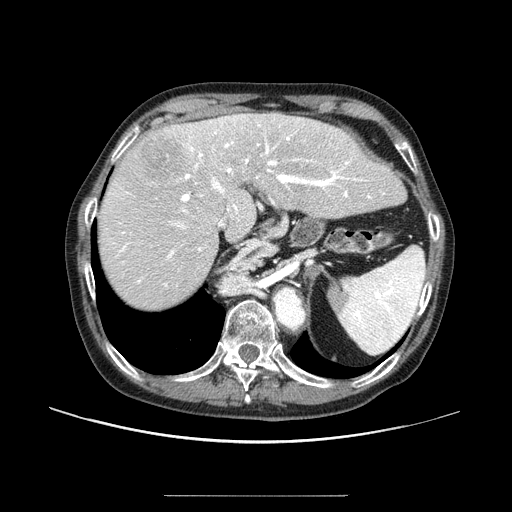
Contrast-enhanced abdominal CT (liver protocol), one axial slice; slice 66 of 91 in the series (ordered by position); reconstruction kernel STANDARD; one of 2 acquisitions stored at this slice position; soft-tissue window (W 400 / L 40 HU); 512 × 512 image matrix, field of view 400 × 400 mm. From the clinical record (not read from this slice): diagnosis: hepatocellular carcinoma (patient treated with transarterial chemoembolisation; whether this scan precedes or follows treatment is not stated here); TNM stage (as recorded): Stage-I; Child-Pugh class: A; tumour differentiation: moderately differentiated; tumour nodularity: uninodular.
Structures marked on this image (semi-automatically segmented with operator editing):
- liver parenchyma outside the tumour (the mass and vessels are separate outlines, so this box may not span the whole liver): bounding box (x1, y1, x2, y2) in pixels: (98, 112, 394, 308)
- mass: (136, 130, 188, 184)
- liver vessels: (118, 115, 353, 287)